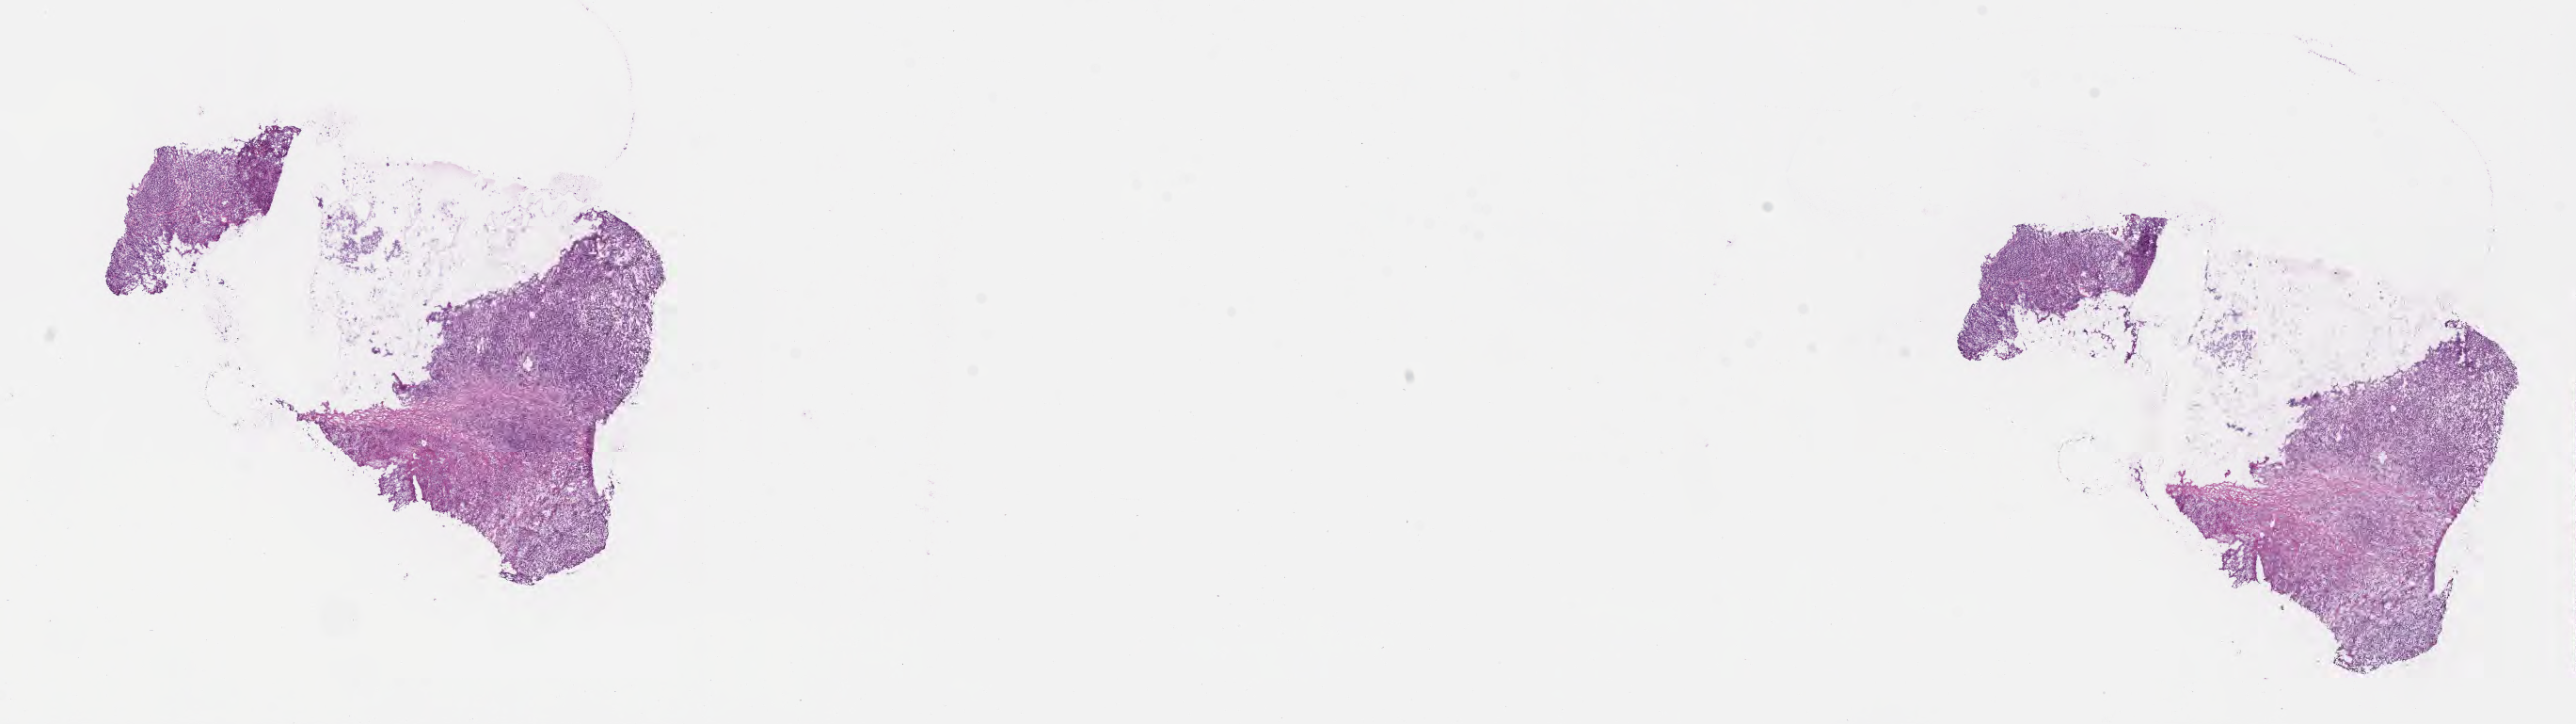
Digitized H&E-stained section — low-resolution overview of the scanned area, about 22.1 x 6.2 mm, frozen section, specimen: metastatic tumor tissue, resected from connective, subcutaneous and other soft tissues. Patient: female, age at initial diagnosis 68 years. Slide review estimates, as recorded: tumor cells 55%, tumor nuclei 92%, stromal cells 44%, necrosis 1%, normal cells 0%. Inflammatory infiltration, as recorded: lymphocyte infiltration 6%, monocyte infiltration 0%, neutrophil infiltration 0%.
Patient diagnosis (primary): Malignant melanoma, NOS.